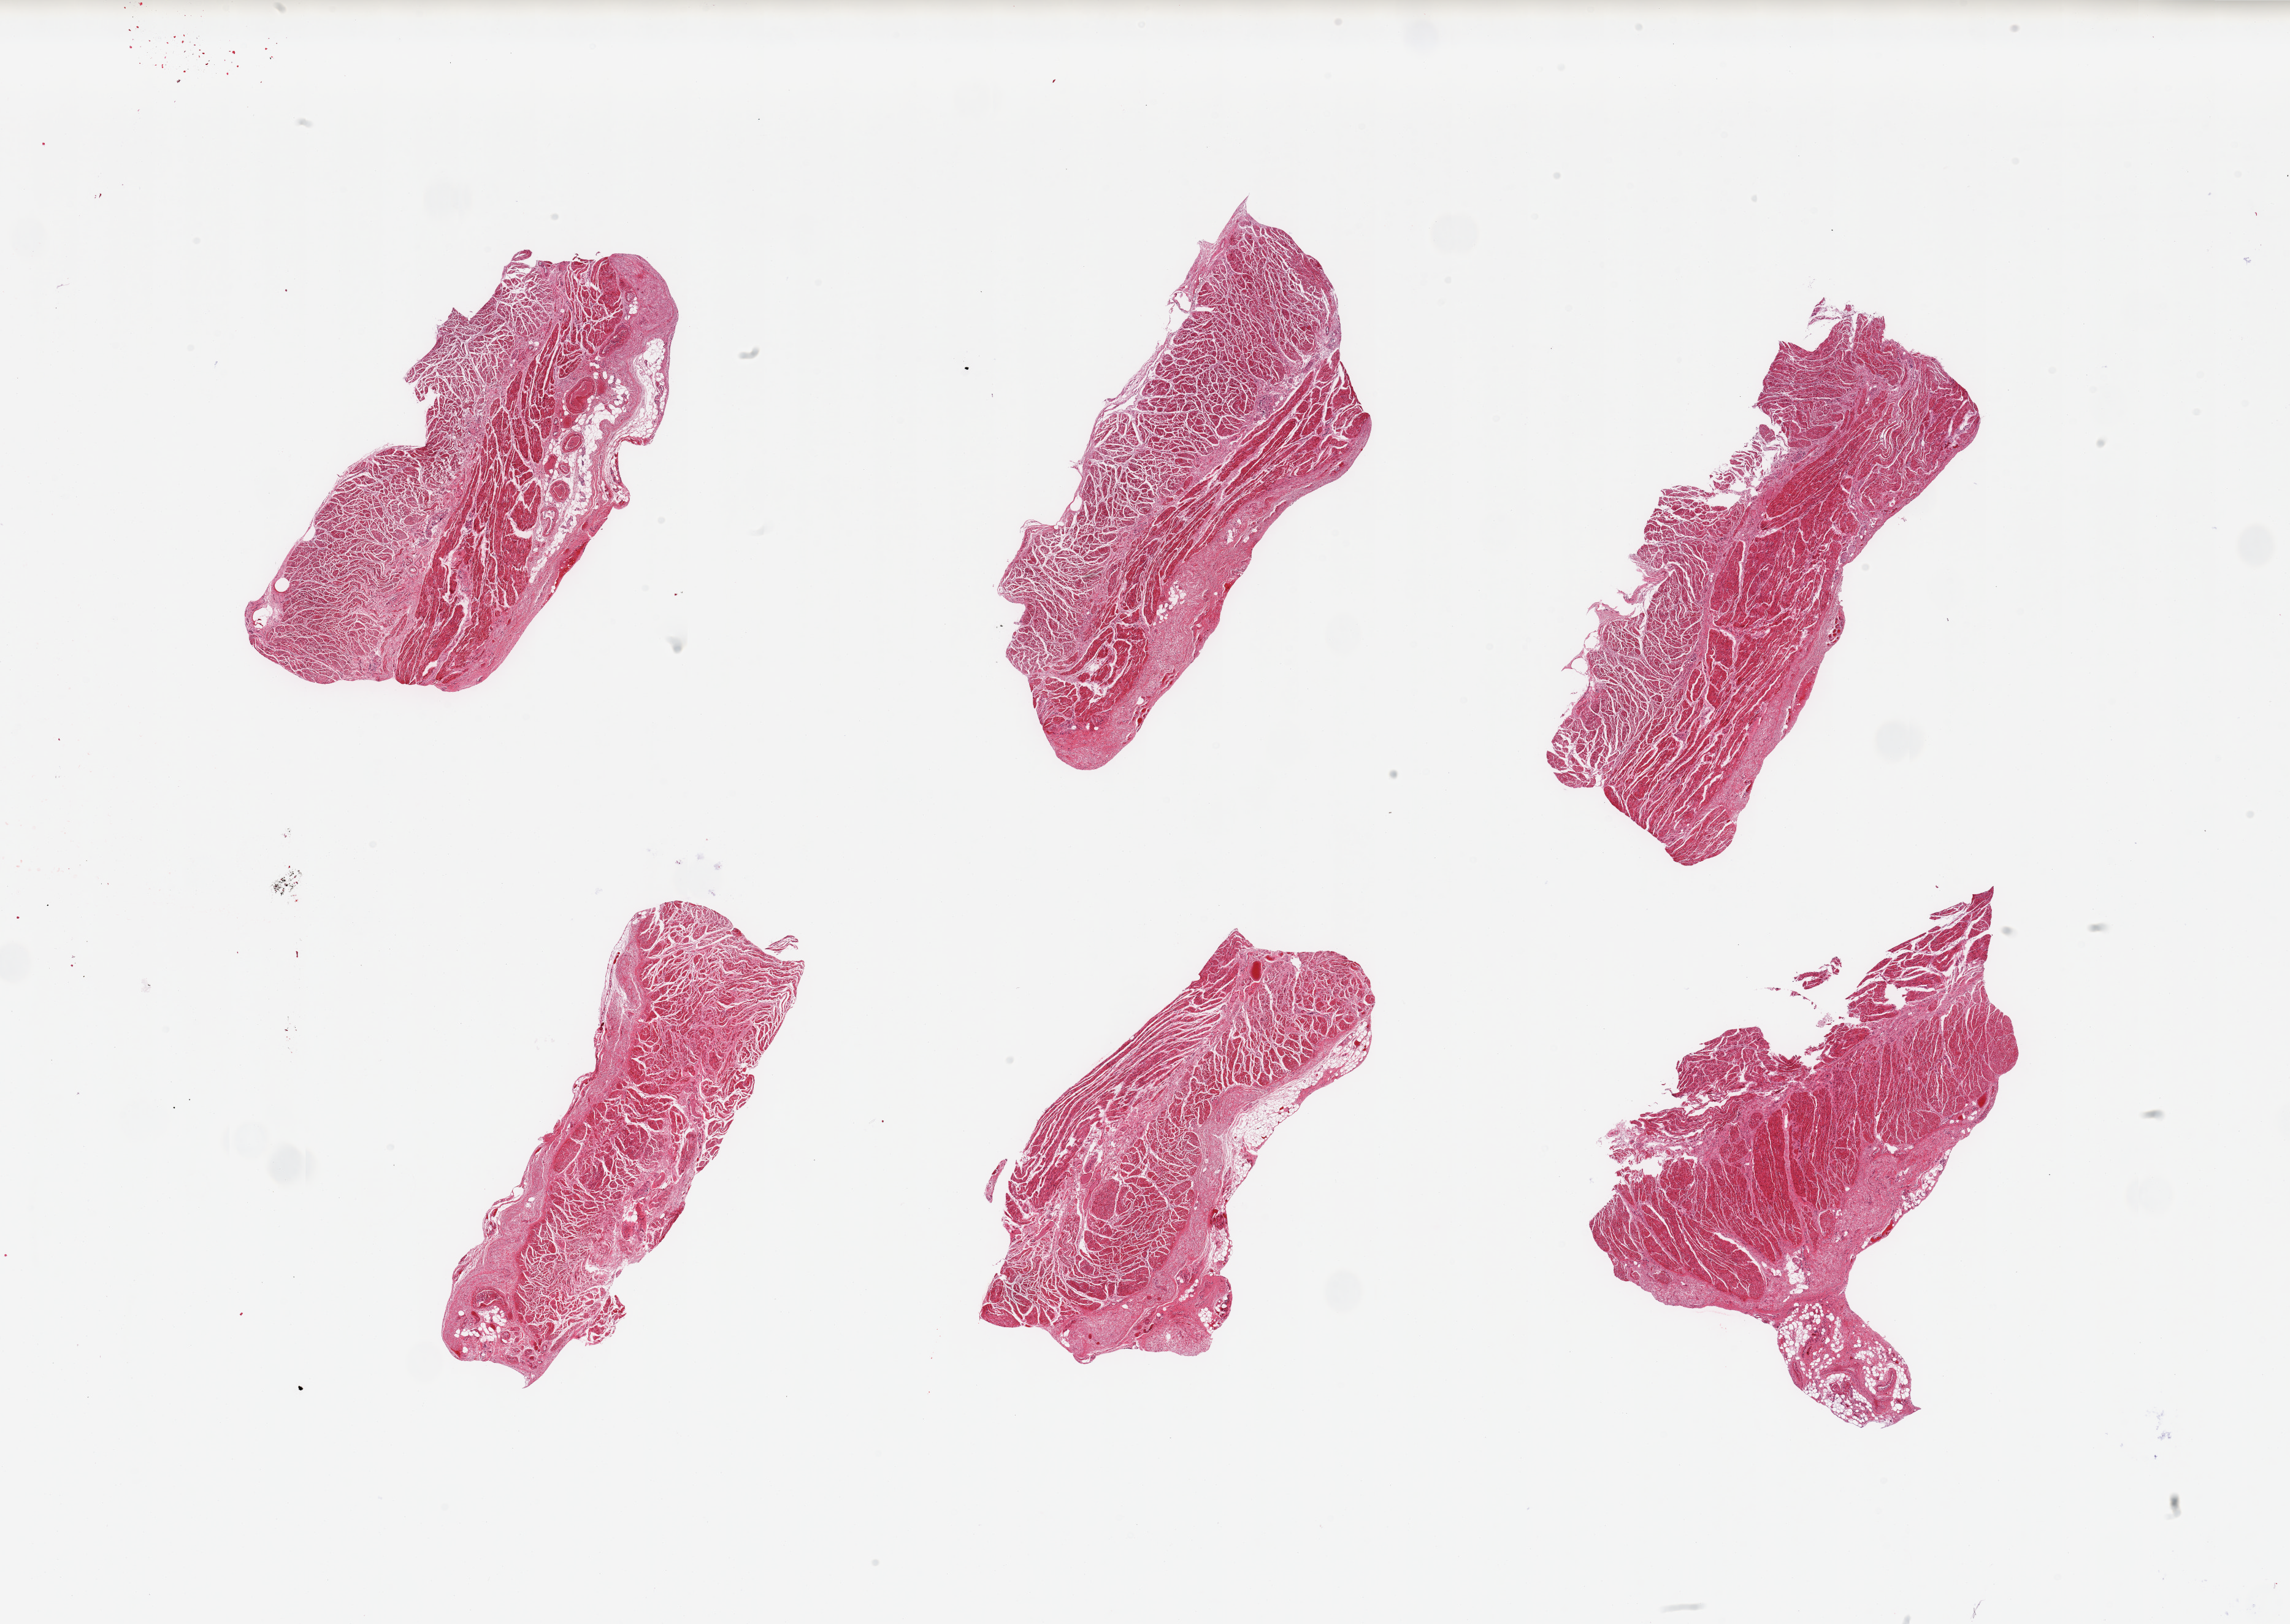
Haematoxylin and eosin whole-slide image, a low-resolution overview of the entire scanned area, about 29.5 x 20.9 mm; PAXgene-fixed, paraffin-embedded tissue; sampled site (target tissue): gastroesophageal junction; tissue donor sample. Female donor.
- reviewer comment on this tissue sample: 6 pieces, confirmed target muscularis